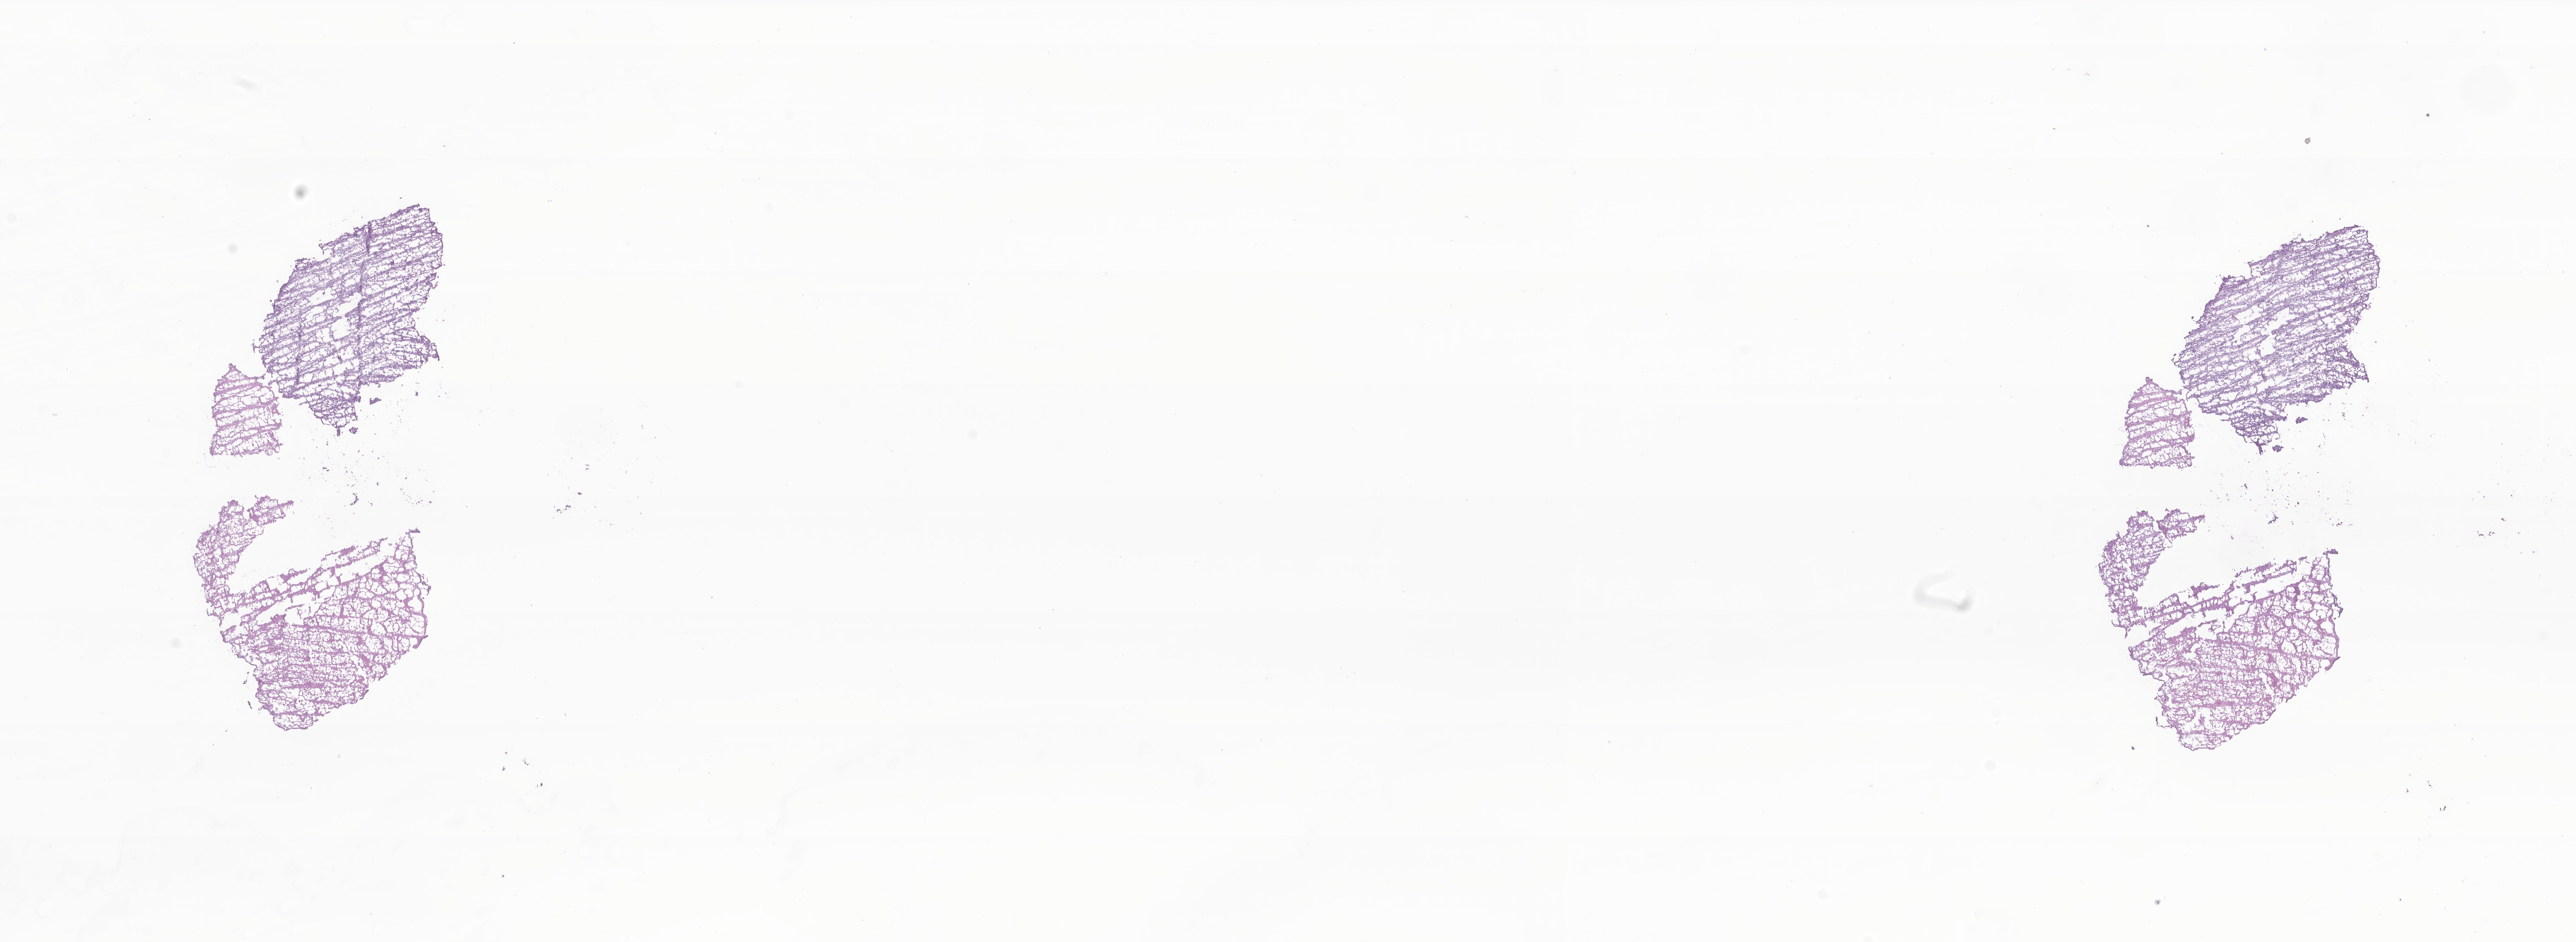
Hematoxylin and eosin (H&E) whole-slide image of tumor tissue from the soft tissue of lower extremity — low-resolution overview of the scanned area, about 24.4 x 8.9 mm. Frozen section (OCT-embedded). Patient: female, age 134 months (11 years 2 months).
Tissue or organ of origin (case record): connective, subcutaneous and other soft tissues of lower limb and hip. Diagnosis: Epithelioid sarcoma, NOS.